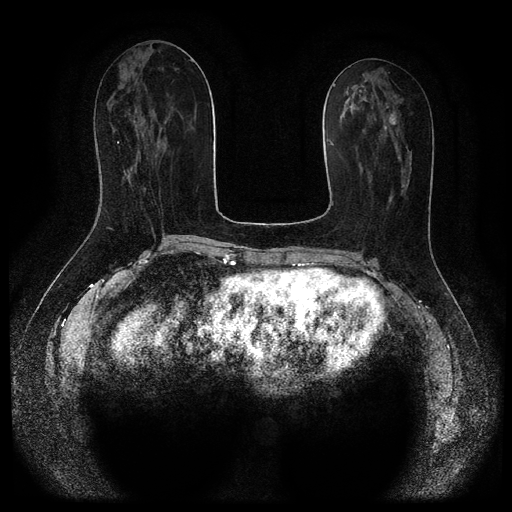
Breast MRI (dynamic contrast-enhanced, multi-phase), one axial slice. Slice 43 of 116 in the series (ordered by position). Dynamic contrast-enhanced series, time point 2 of 5 at this slice position (early post-contrast). 1.5 T. TE 2.7 ms, TR 5.4 ms. 2 mm slice thickness. 512 × 512 image matrix. Patient: female, 47 years.
Structures marked on this image (semi-automatically segmented with operator editing):
- breast lesion (labelled benign in the annotation): bounding box [x1, y1, x2, y2] px = [389, 114, 397, 125]